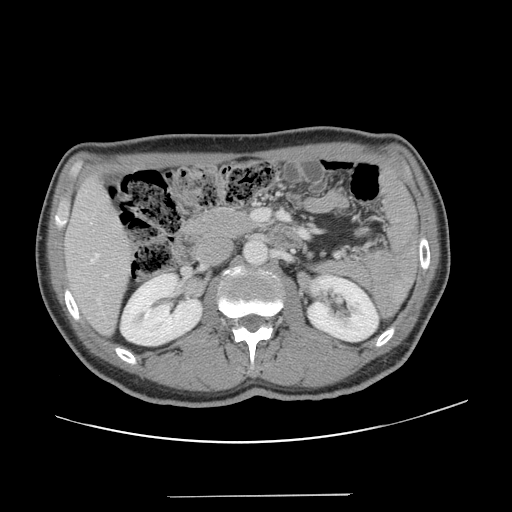
Contrast-enhanced abdominal CT, one axial slice; intravenous contrast given; soft-tissue window (W 400 / L 40 HU); 512 × 512 image matrix. Male patient, age 60 years. From the clinical record (not read from this slice): diagnosis: colorectal cancer liver metastases, imaged before liver resection; multiple liver metastases: no; largest metastasis: 2.5 cm; disease in both lobes: no.
Structures marked on this image (expert manual segmentation):
- hepatic veins: bounding box [x1, y1, x2, y2] px = [91, 223, 99, 263]
- liver: [66, 180, 129, 334]
- planned liver remnant (the part of the liver to remain after resection): [66, 180, 129, 334]